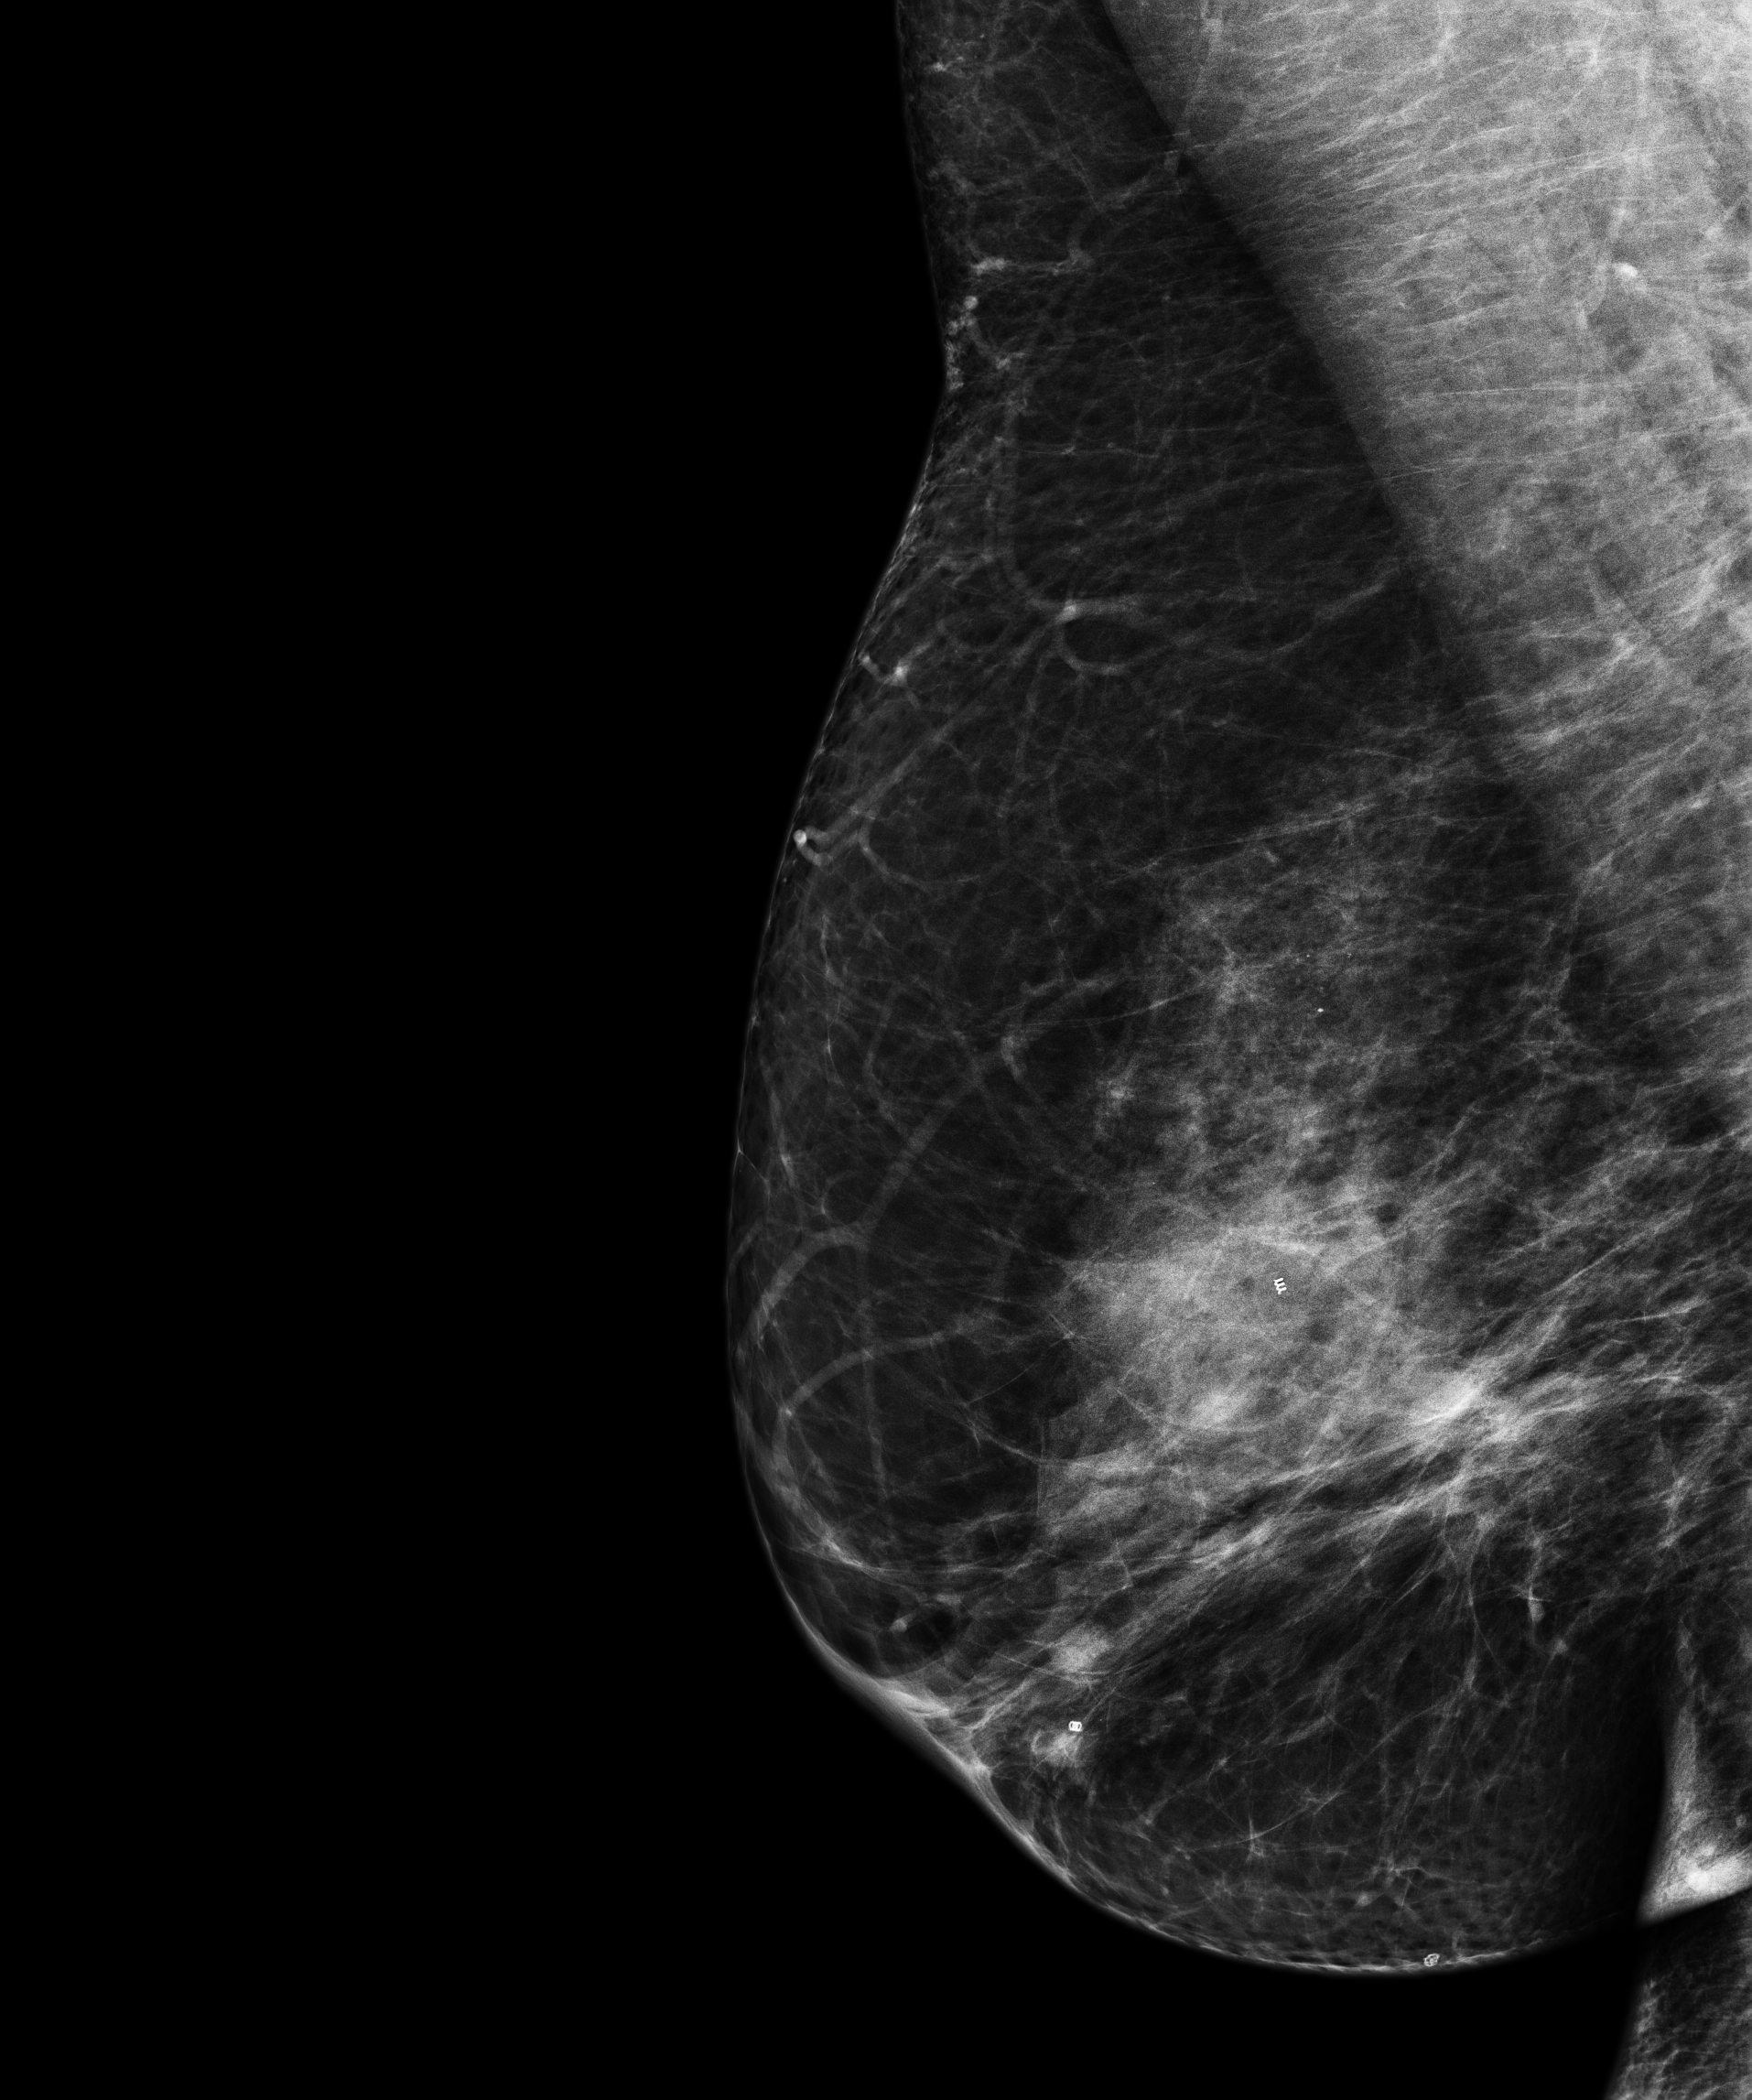
Annual screening mammography examination; compressed breast thickness 83.7 mm; system: Senographe Pristina. Patient: female, 48 years.
Image type: full-field digital mammogram. Breast: right. Projection: mediolateral oblique (MLO) view.